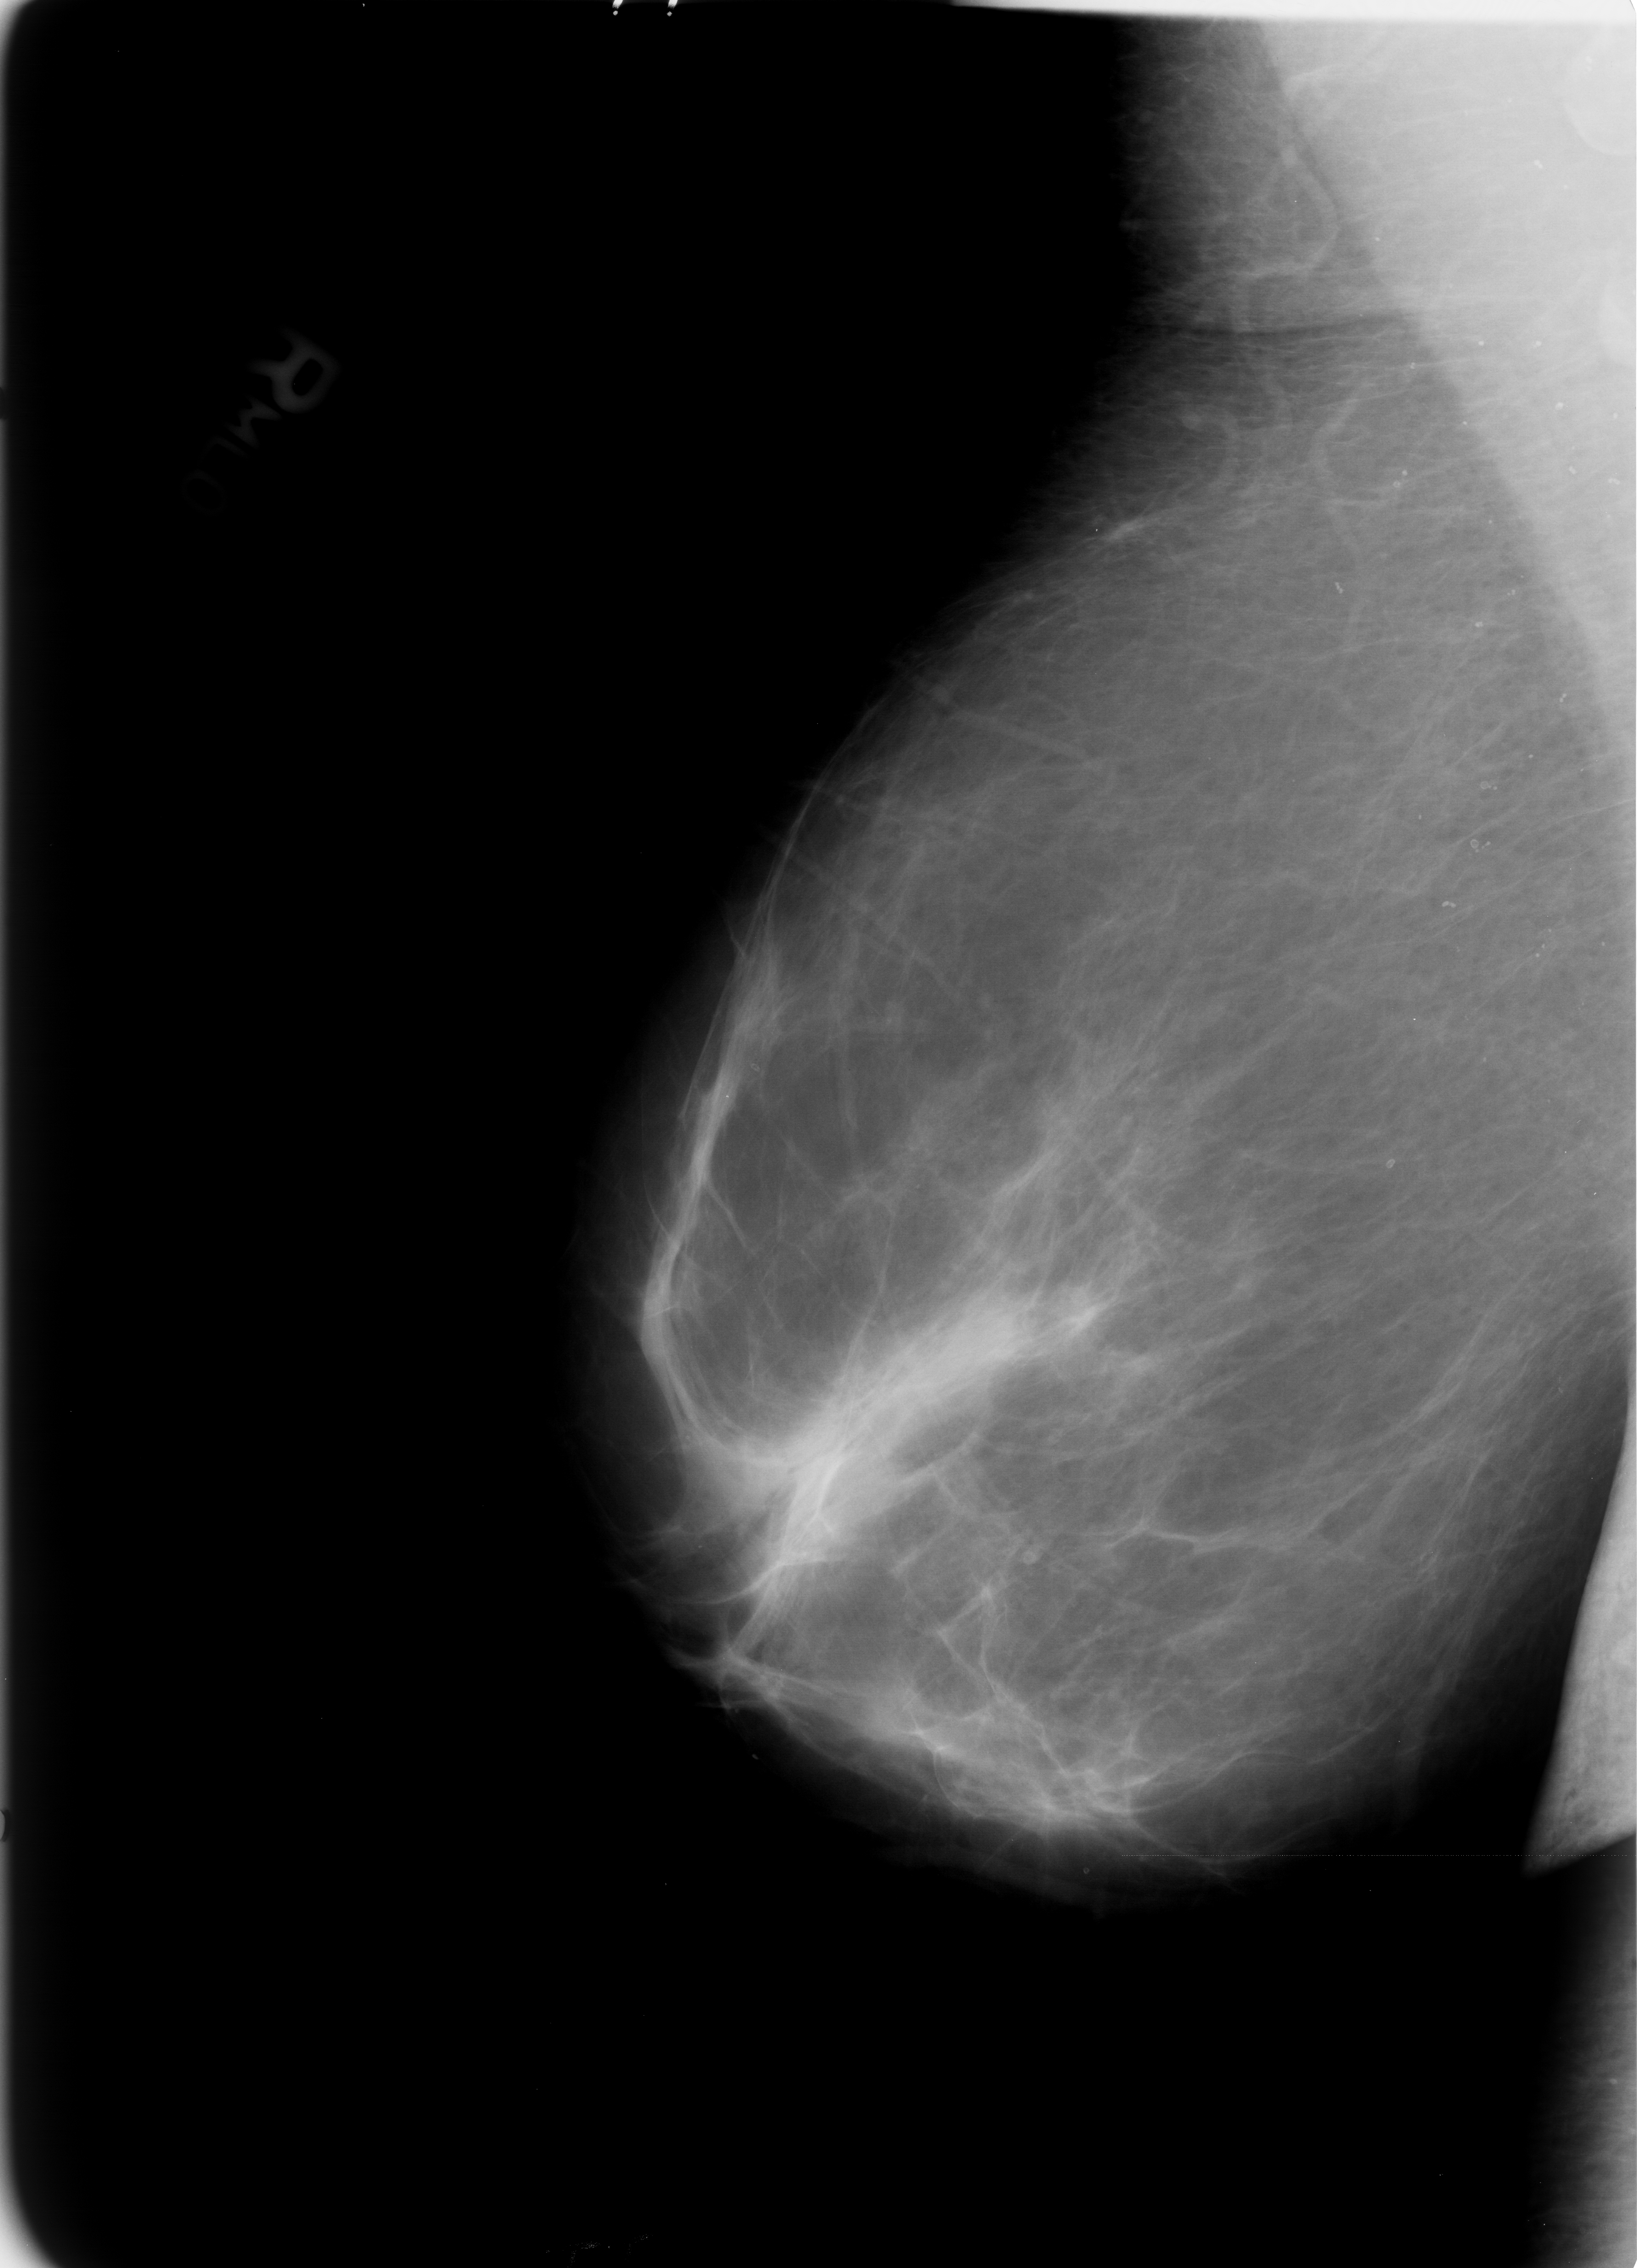
Mammogram (digitized film); right breast; MLO view; BI-RADS breast density category 2 (scale 1–4); 1637 × 2268 image matrix.
Marked abnormalities (boxes around the expert regions of interest):
- calcifications, morphology skin, distribution regional; BI-RADS assessment category 2; benign; no additional work-up was recommended (outcome (as recorded, no biopsy): benign without callback): bounding box [x1, y1, x2, y2] px = [1452, 827, 1495, 861]